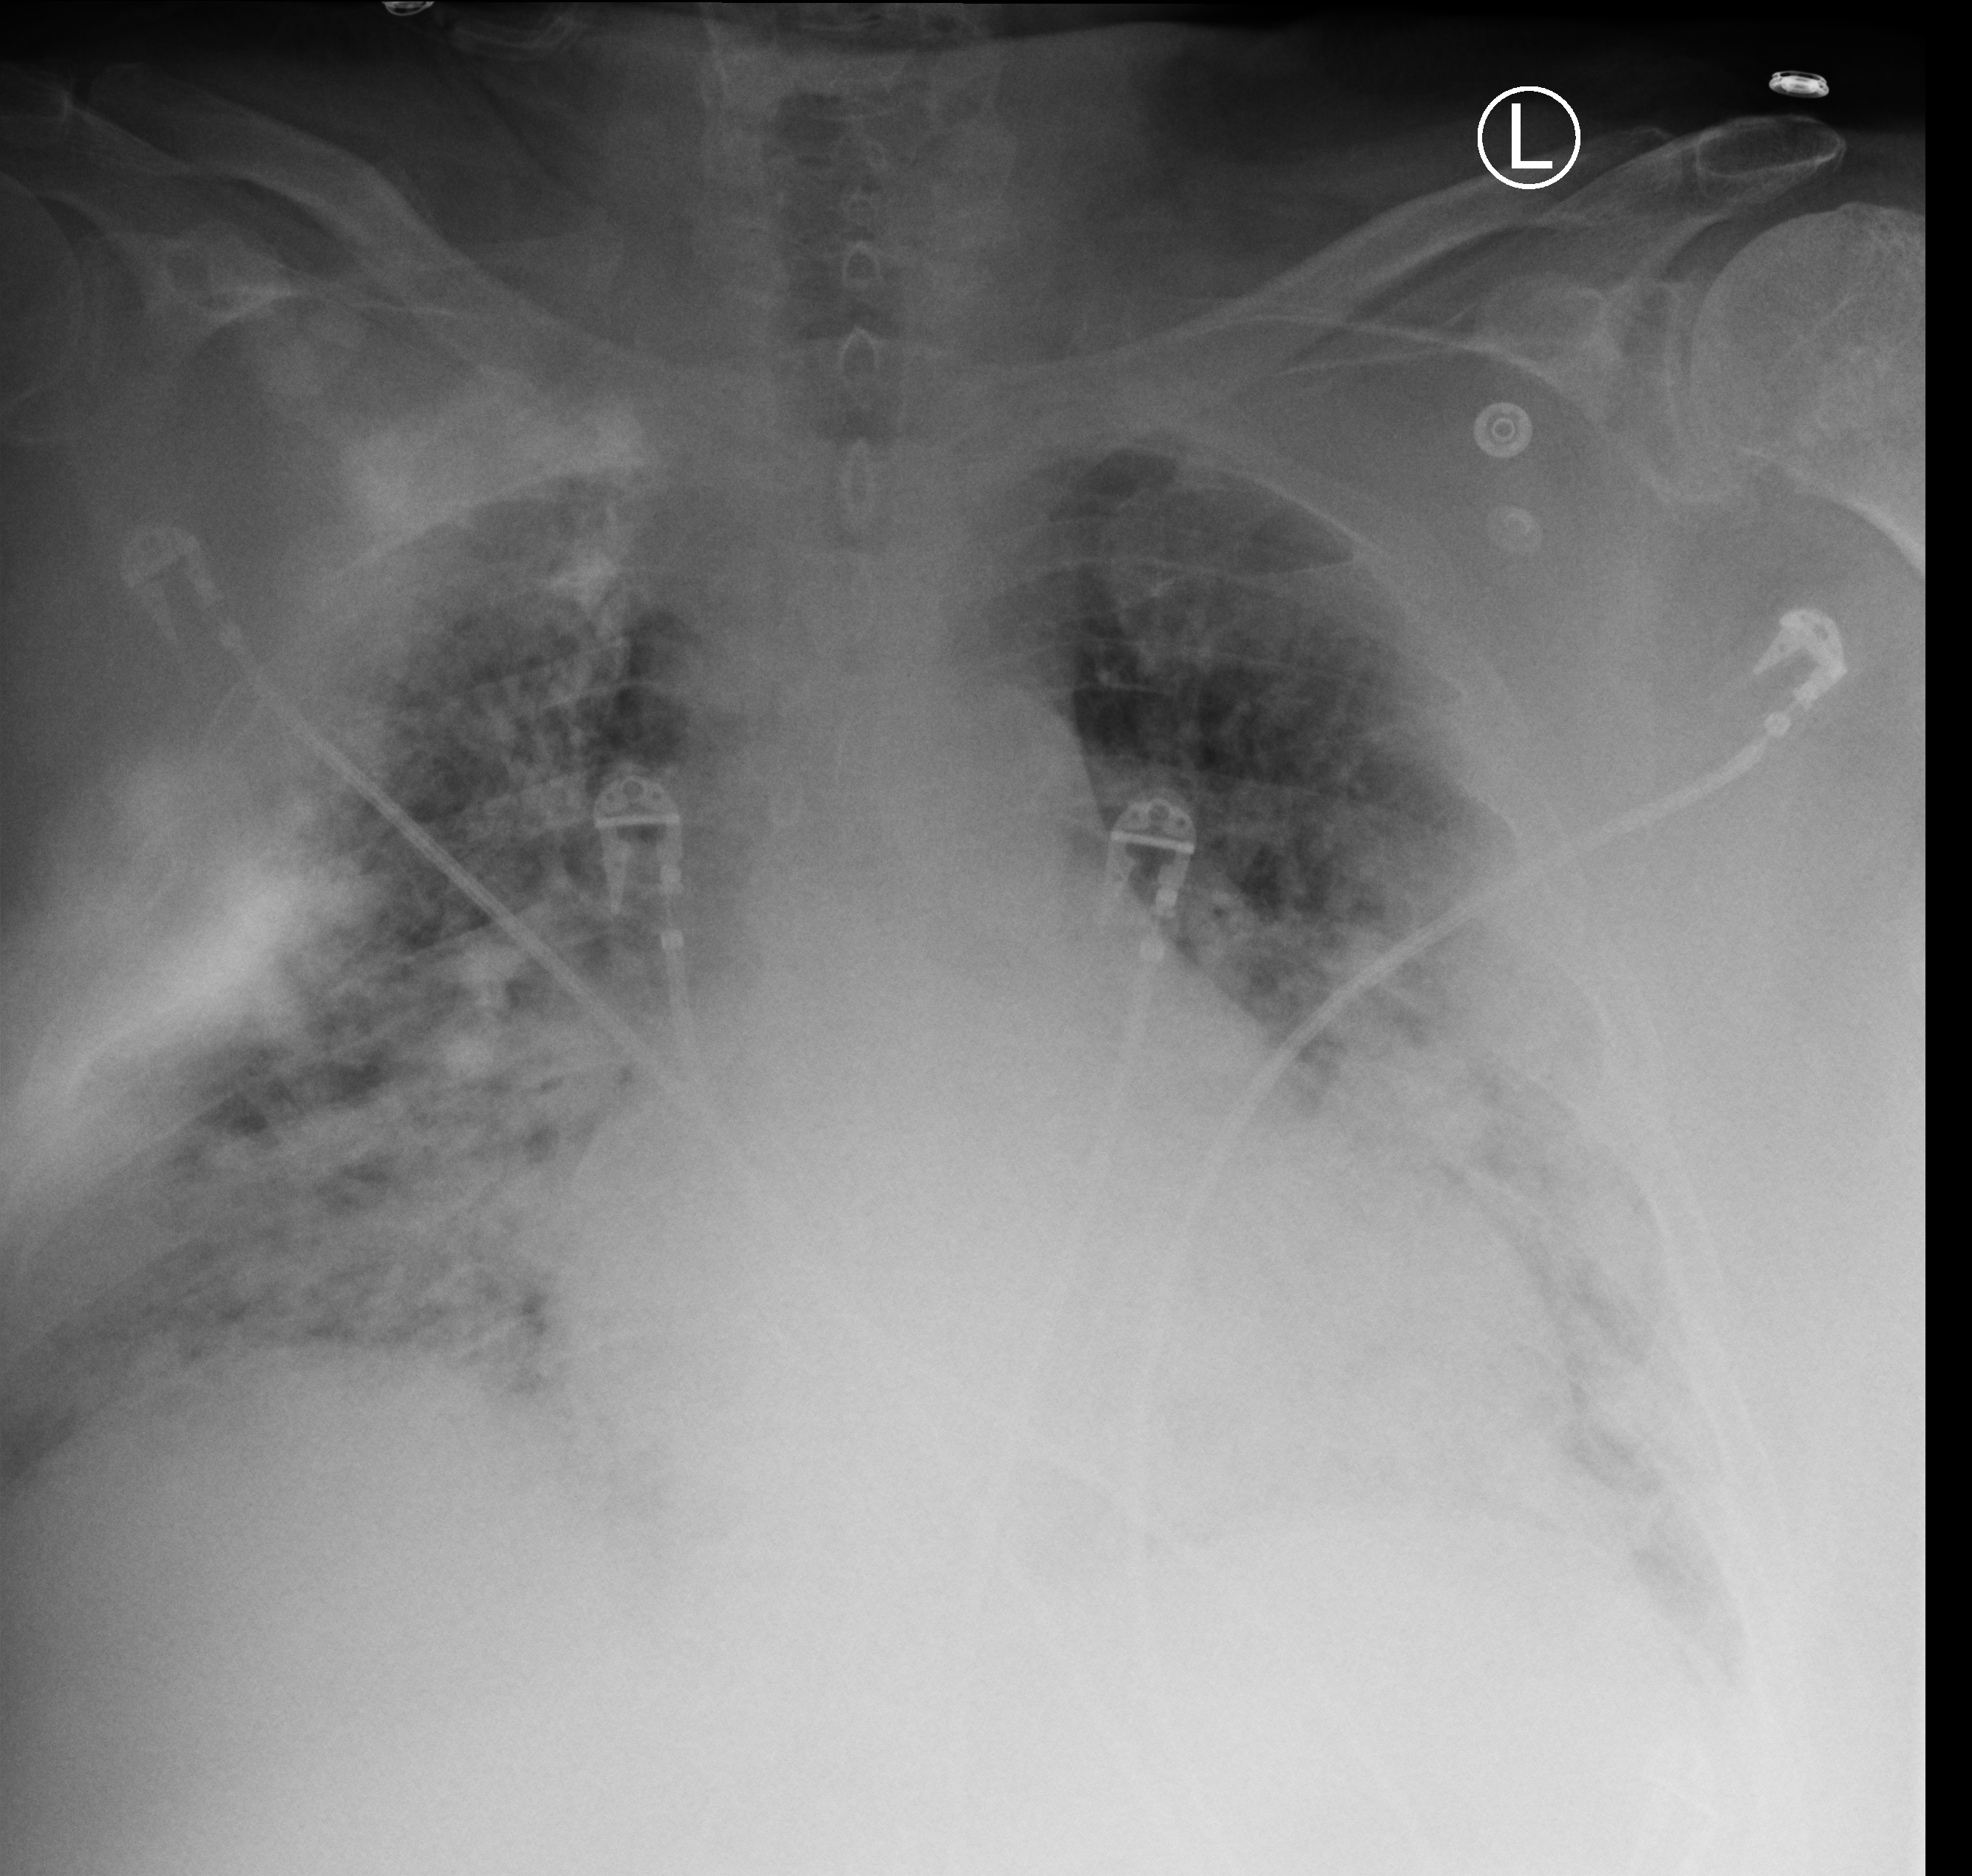
Chest X-ray (portable). Patient hospitalised with COVID-19; male, aged 60–74 years.
From the hospital-stay record, not from the radiograph (when in the stay this image was taken is not recorded):
- mechanically ventilated during this hospital stay: yes
- COPD (admission record): no